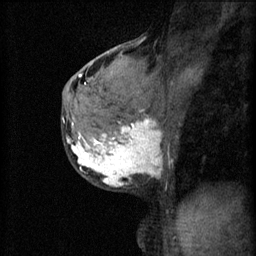
Breast MRI (dynamic contrast-enhanced), one sagittal slice; position 35 of 60 along the scan axis; 3 images stored at this slice position (order not interpretable as contrast timing); 1.5 T; TE 4.2 ms, TR 11 ms; 2 mm slice thickness; 256 × 256 image matrix, field of view 180 × 180 mm. Patient: female, 37 years.
Annotated regions visible in this slice (semi-automatic segmentation, software-assisted and operator-edited):
- analysis volume of interest (the breast-tissue region the enhancement analysis was run in; not a lesion): box from (x=68, y=118) to (x=175, y=191) px
- tumour enhancement mask (voxels above the 70 % enhancement threshold inside the analysis volume of interest): (x=68, y=118)–(x=162, y=187)